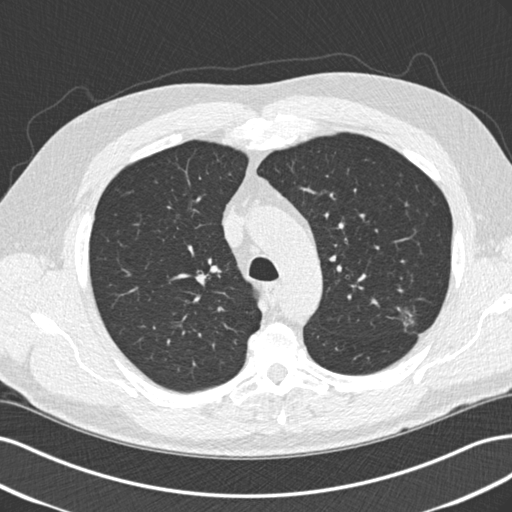
Low-dose screening chest CT, one axial slice; position 157 of 209 along the scan axis; reconstruction kernel B30f; 120 kVp; lung window (W 1500 / L -600 HU); 2 mm slice thickness; 512 × 512 image matrix.
Outlined on this slice (manually delineated by an expert):
- lesion 1 (tumor, upper lobe of left lung): bounding box (x1, y1, x2, y2) in pixels: (402, 310, 414, 326)